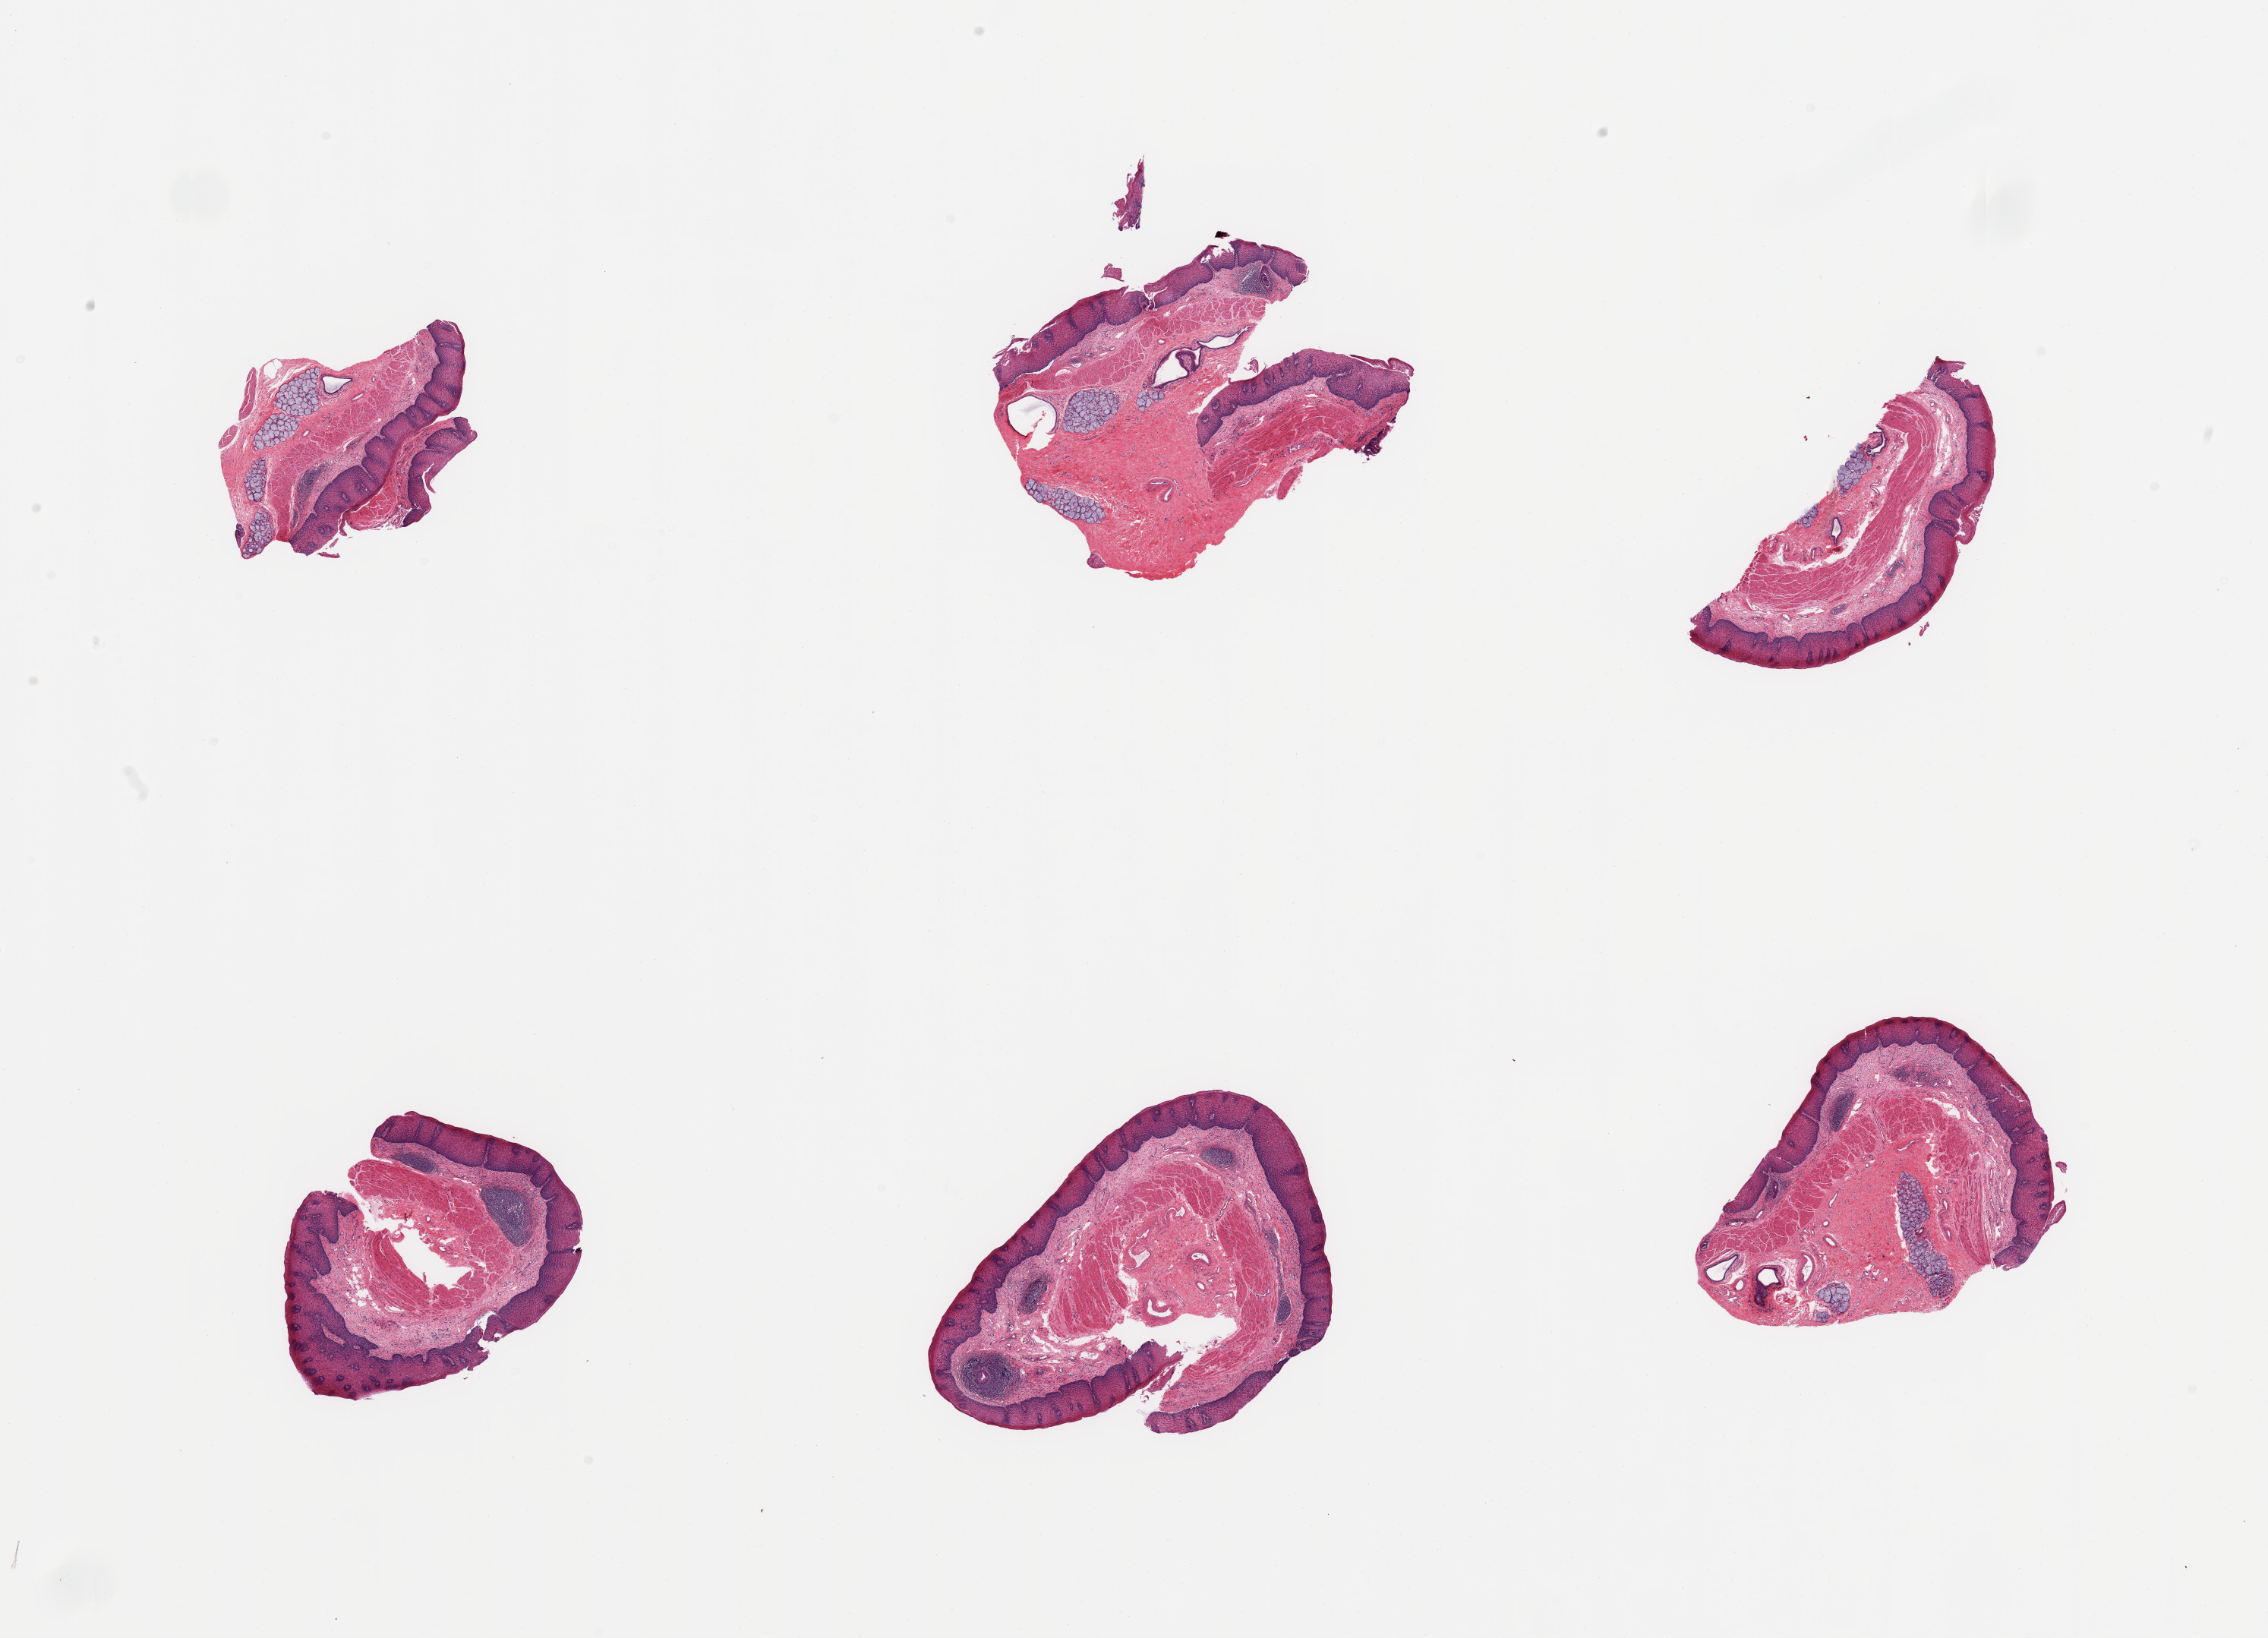
Hematoxylin and eosin (H&E) whole-slide image, shown as a low-resolution overview of the whole scanned area (about 23.6 x 17.1 mm), PAXgene-fixed paraffin-embedded (PFPE) section, sampled site (target tissue): esophageal mucous membrane, tissue donor sample. Male donor.
Pathologist's review note for this sample: 6 pieces; includes several clusters of submucosal glands and few lymphoid aggregates.